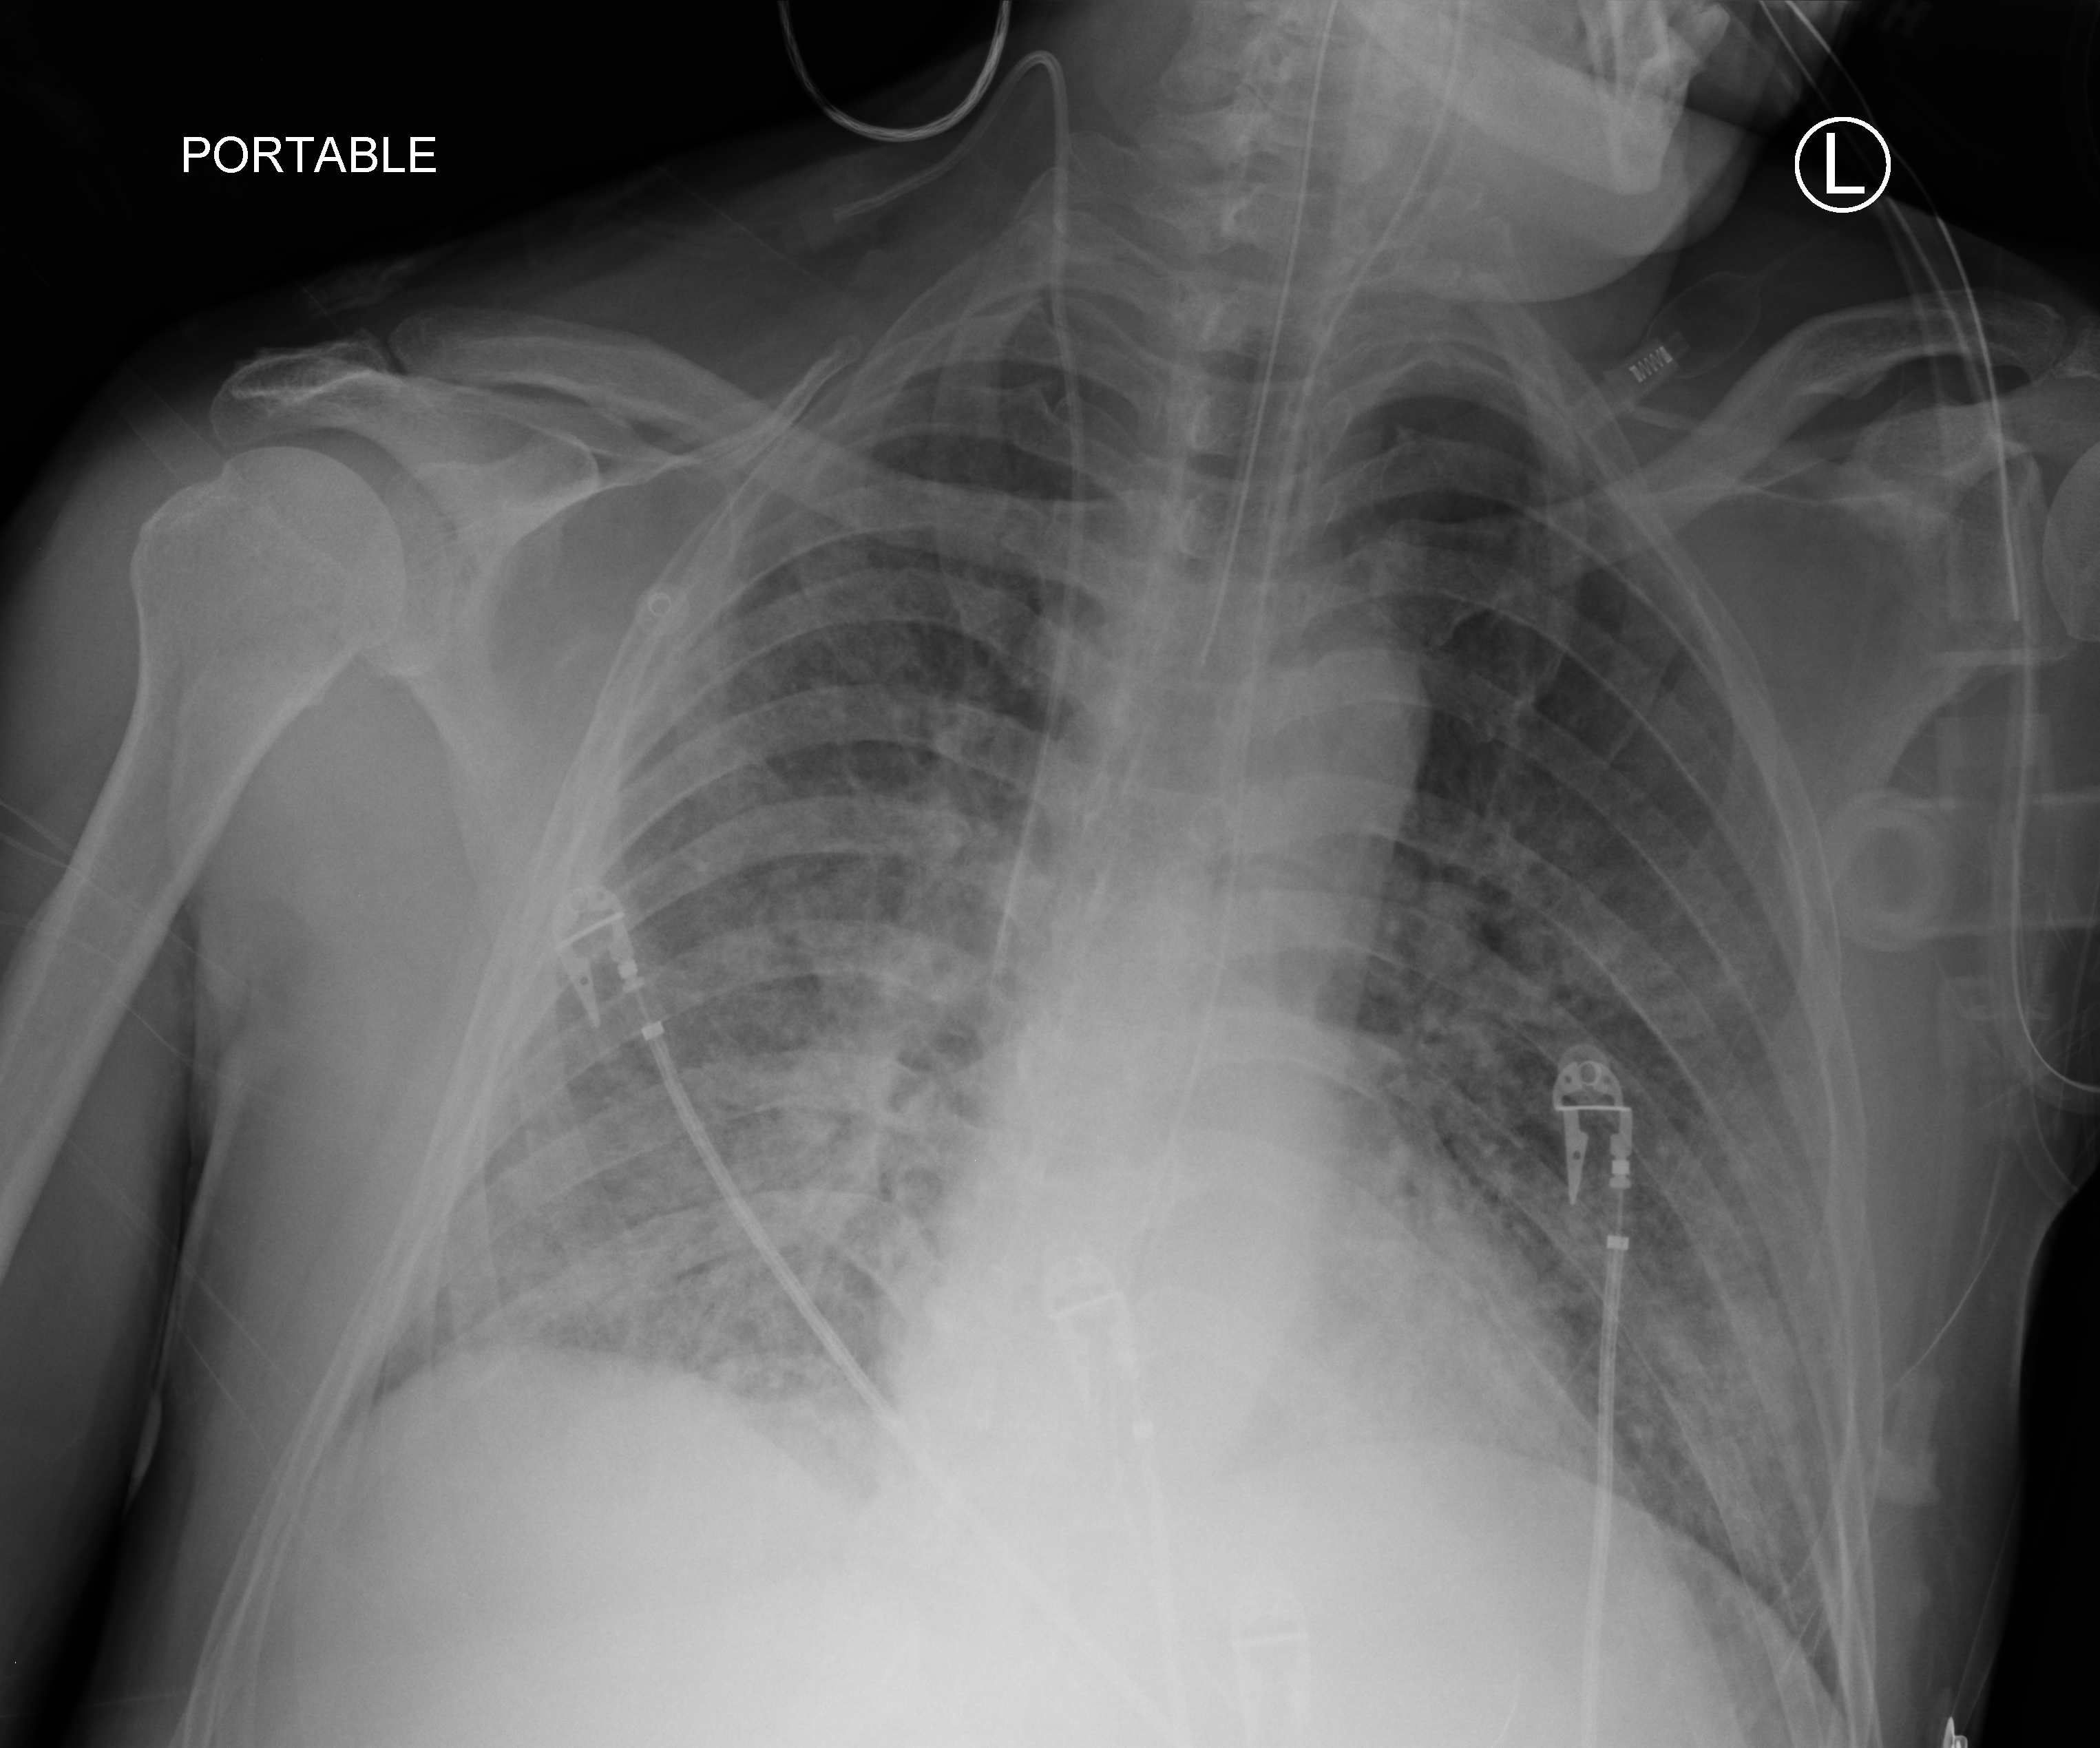
Bedside chest radiograph (computed radiography). Patient hospitalised with COVID-19; male, aged 60–74 years.
Hospital-stay facts (about this admission, not read from this image; timing relative to this image not recorded): other chronic lung disease (admission record): no; mechanically ventilated during this hospital stay: yes; admitted to intensive care during this hospital stay: yes.